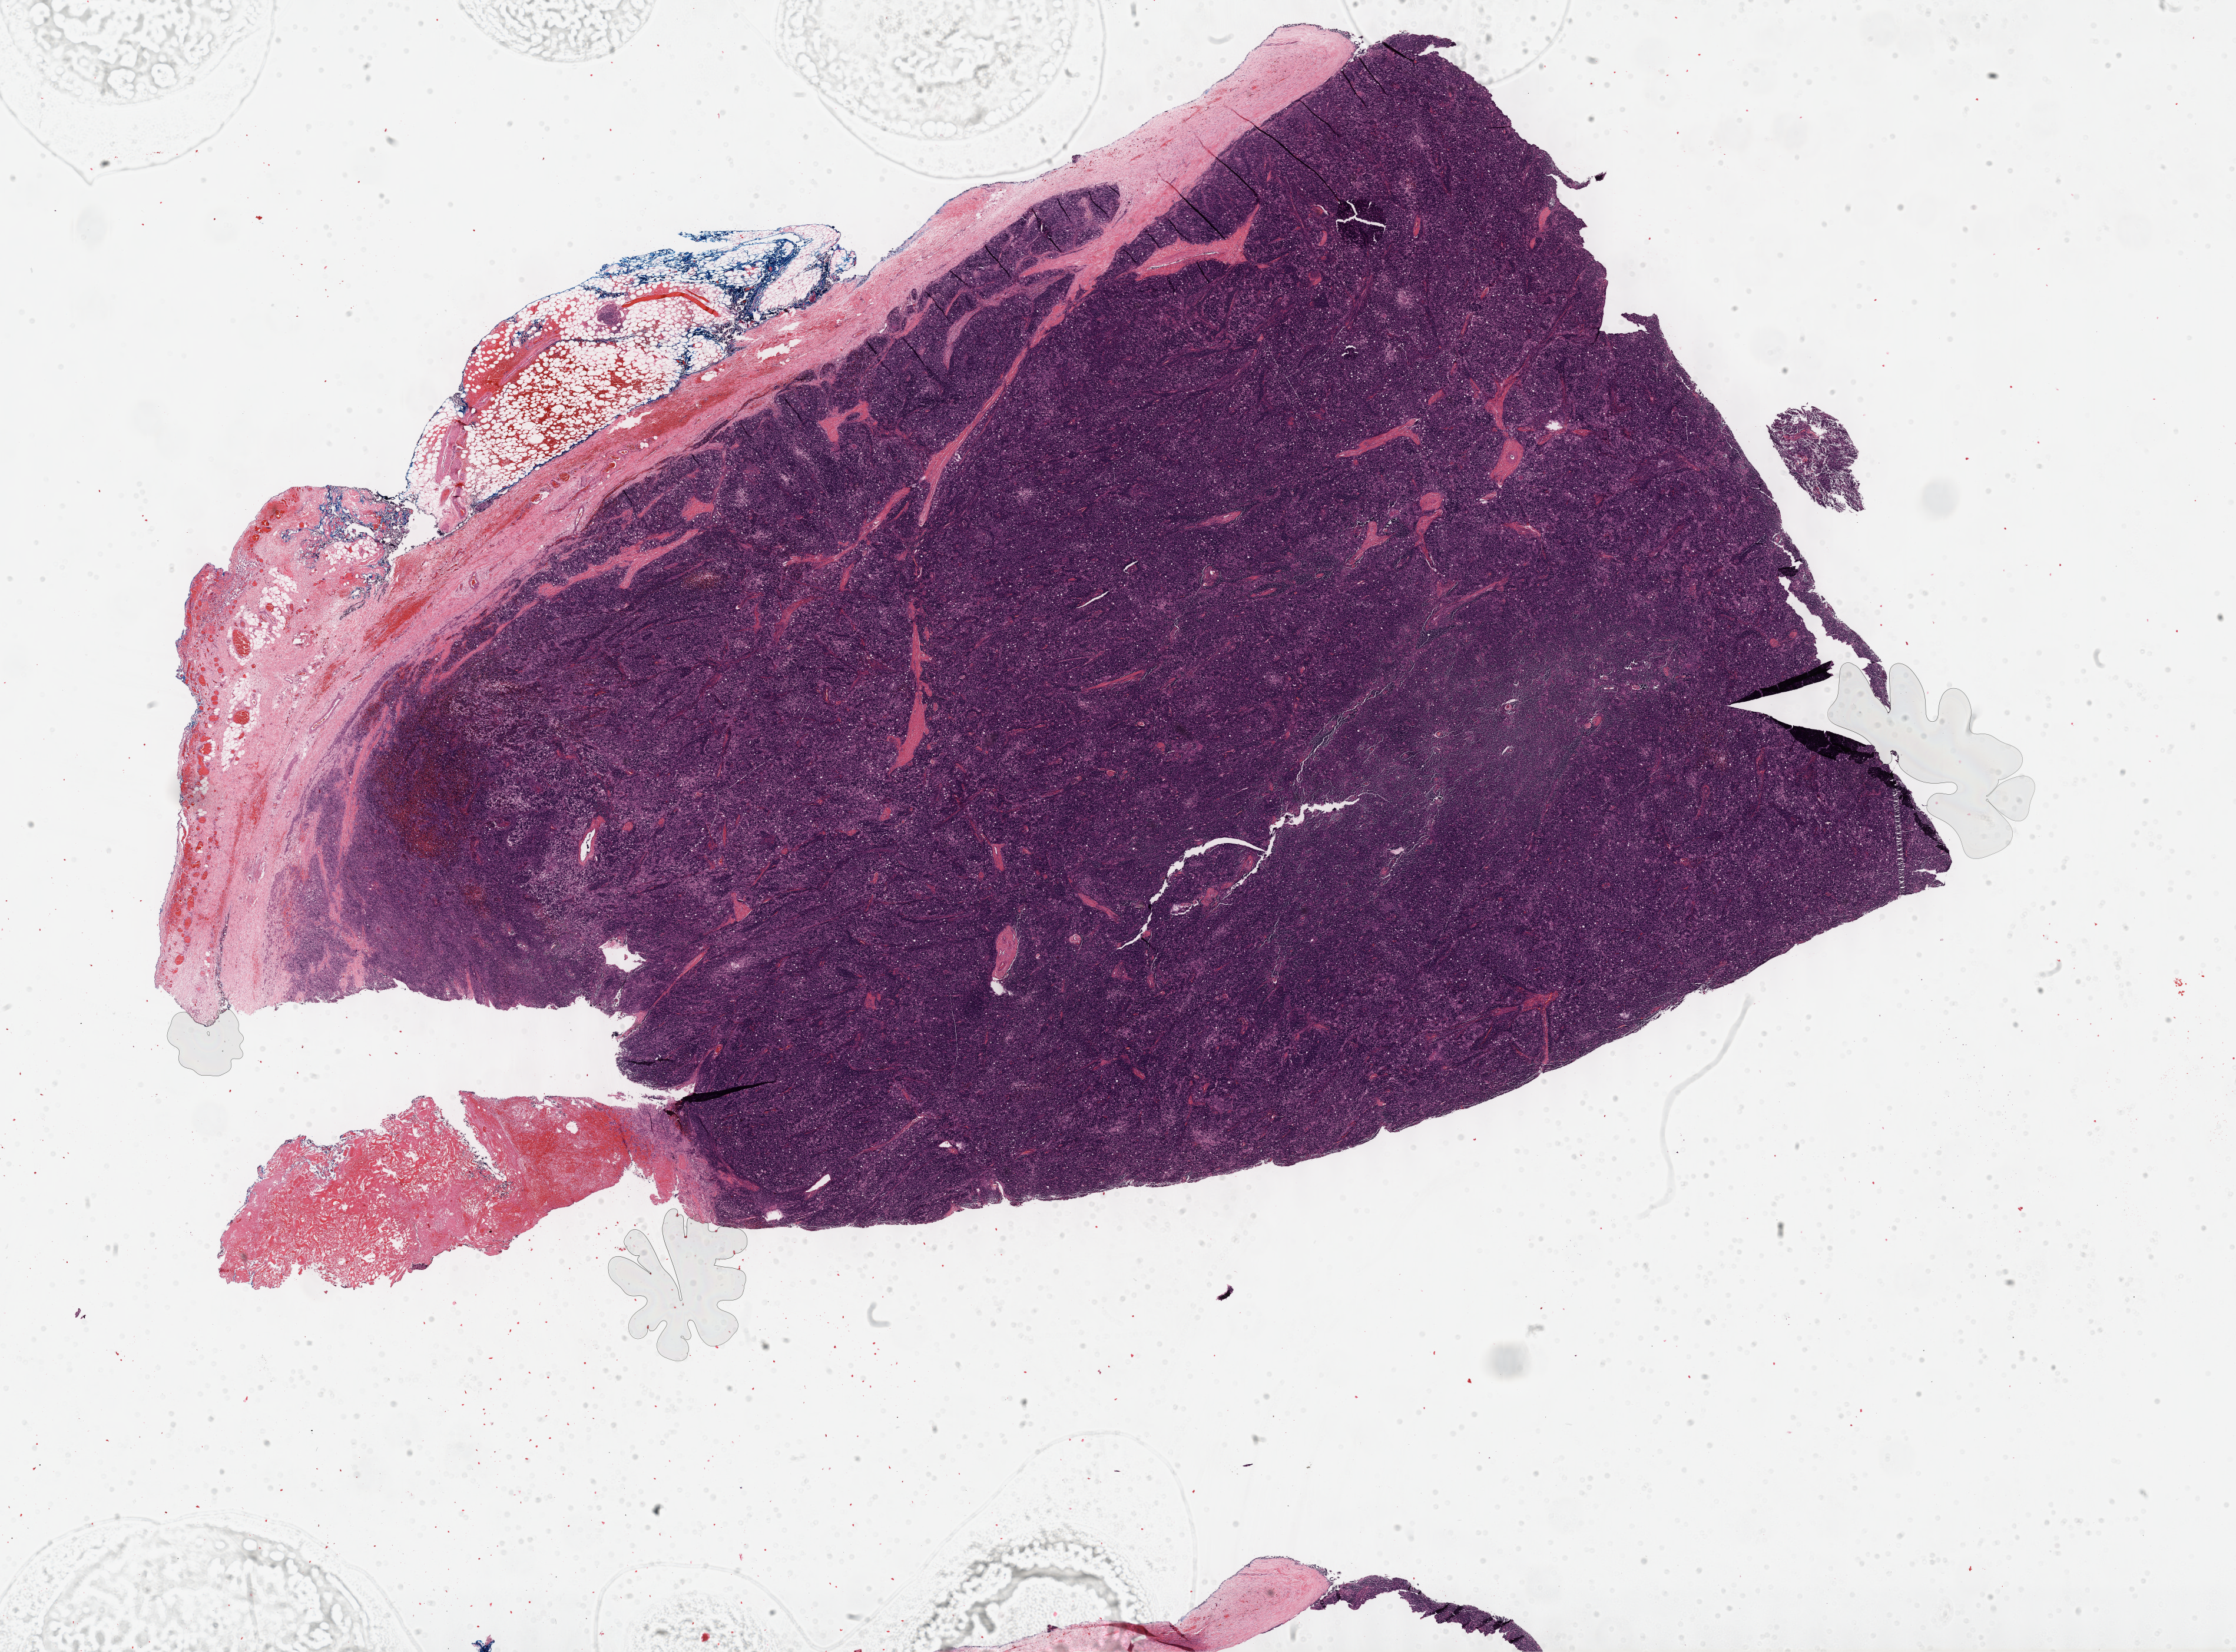
H&E whole-slide image — a low-resolution overview of the entire scanned area, about 30.7 x 22.7 mm (from a 40x scan), formalin-fixed paraffin-embedded (FFPE) diagnostic section, thymus, primary tumour sample. Patient: male, age at initial diagnosis 43 years.
Diagnosis: Thymoma, type B2, malignant.